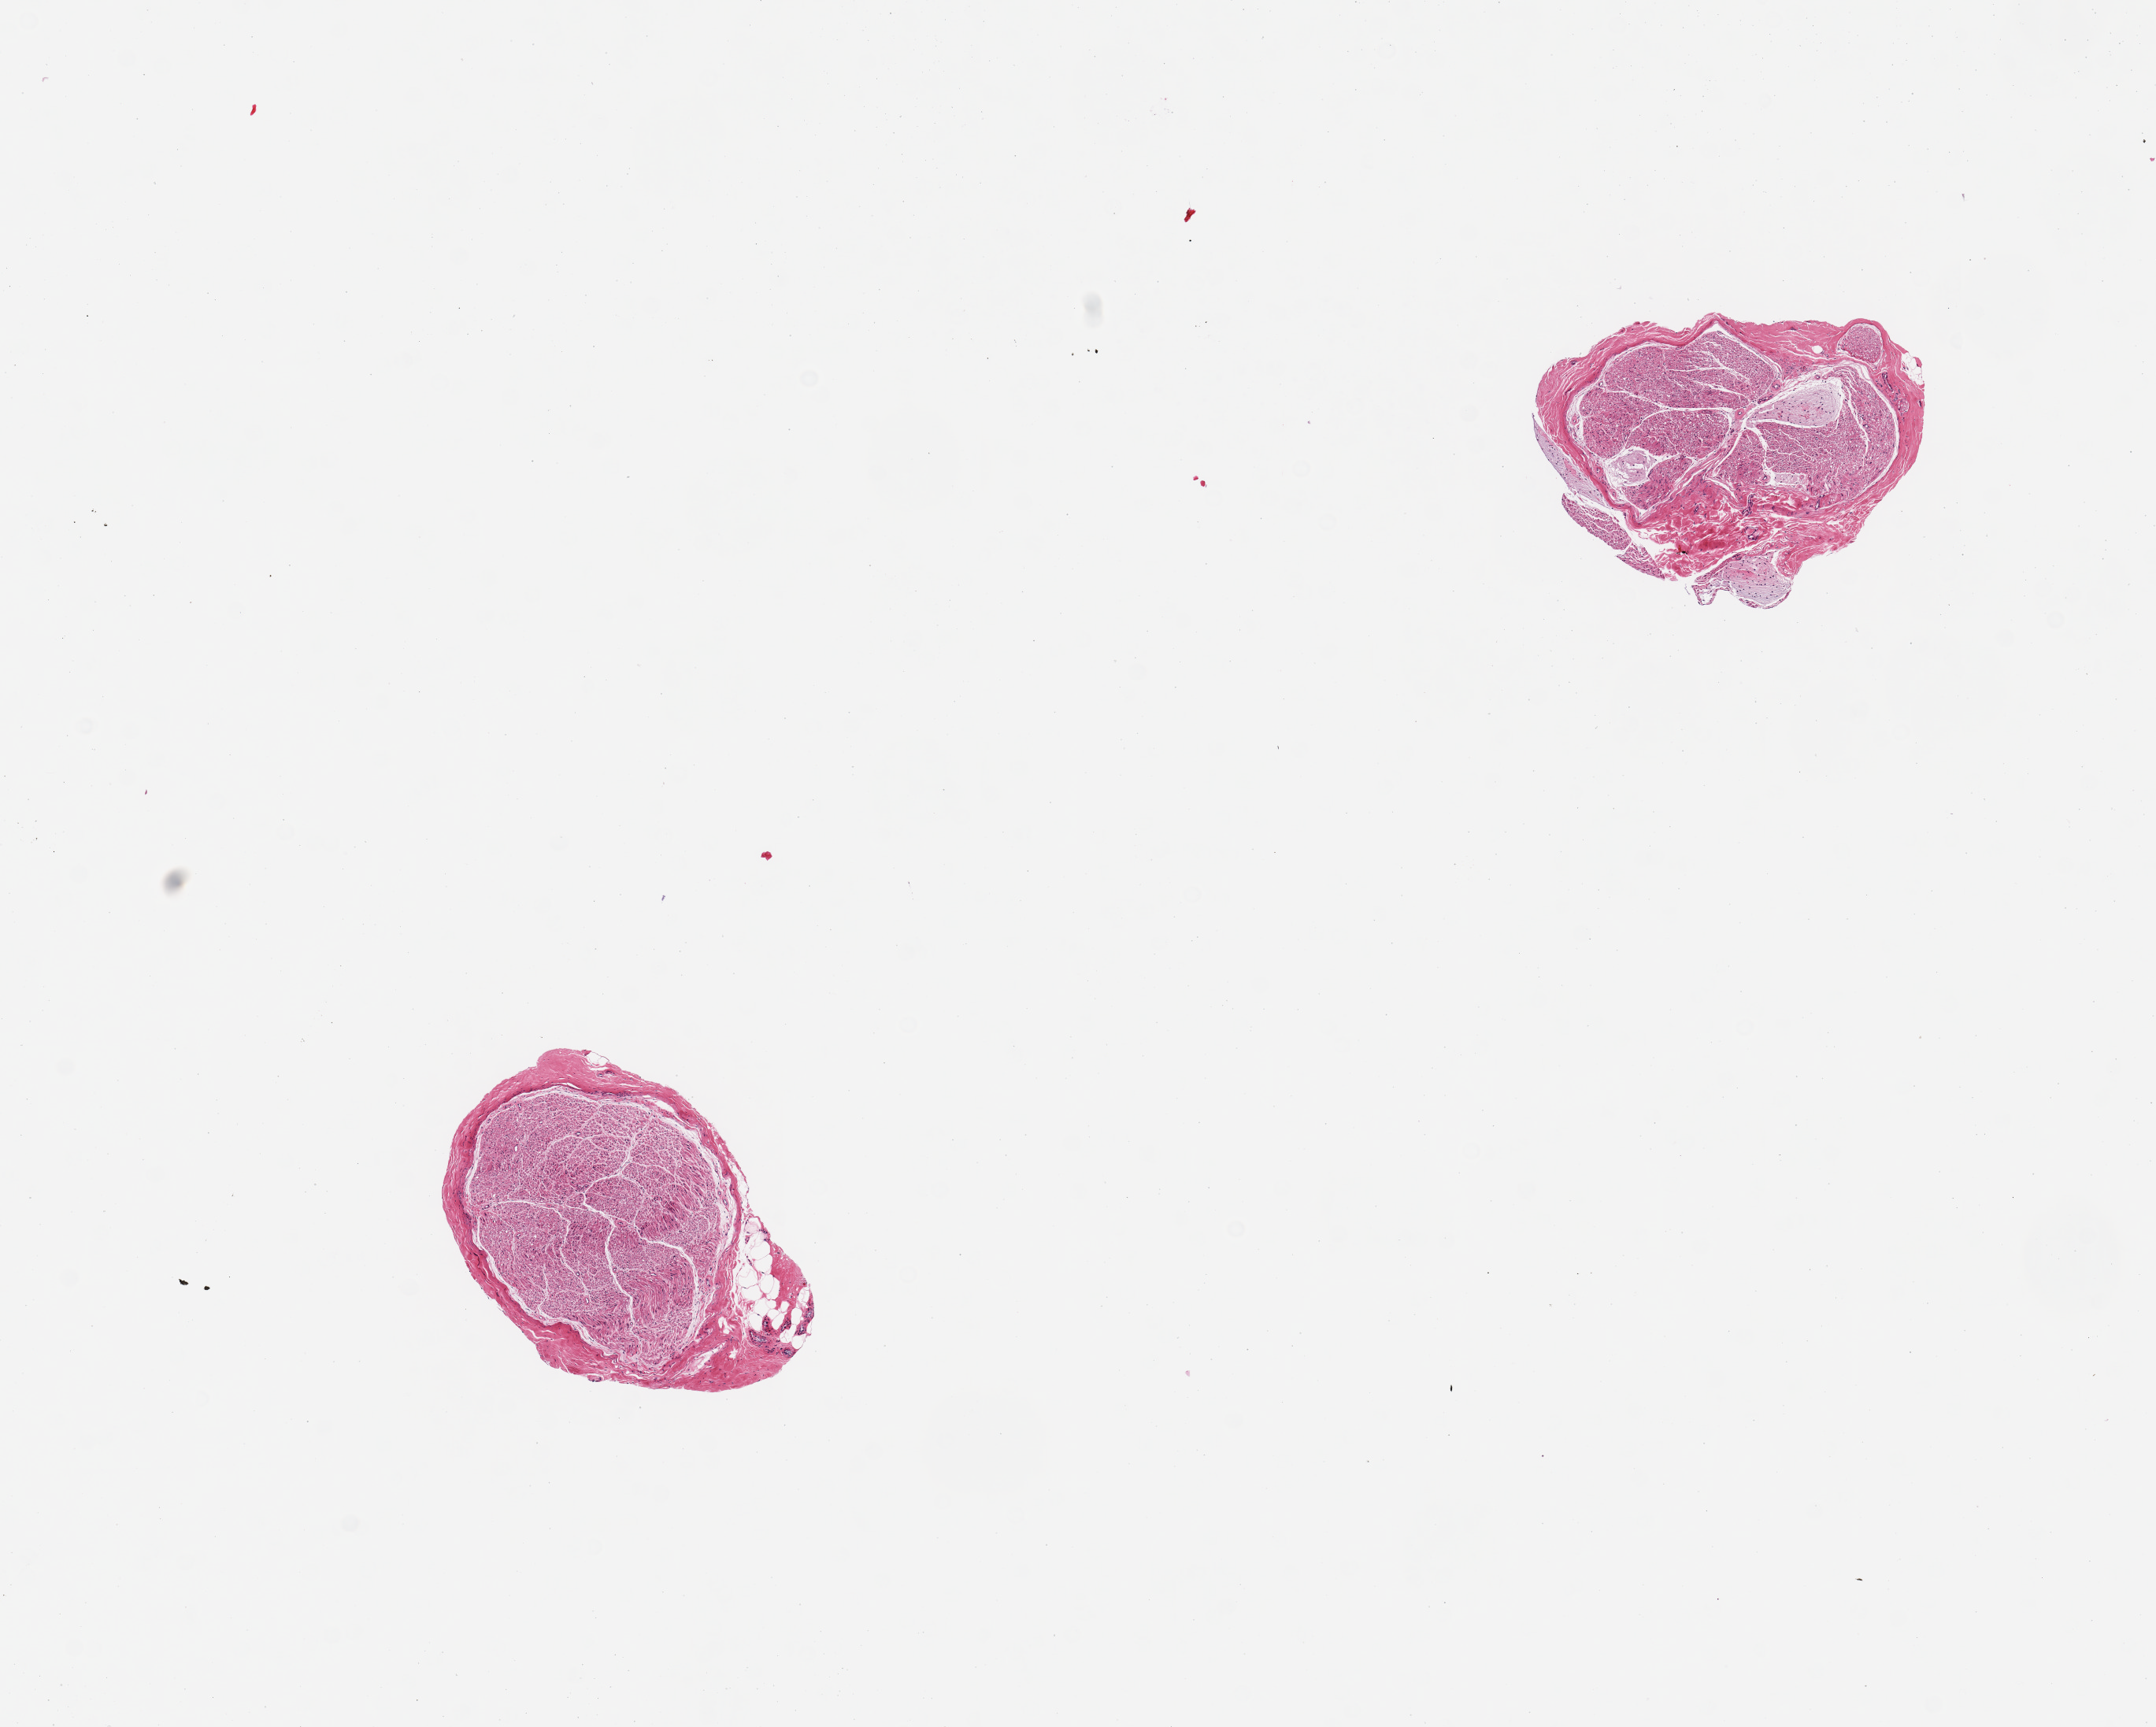
H&E whole-slide image, brightfield — shown as a low-resolution overview of the whole scanned area (about 10.8 x 8.7 mm, acquisition: 20x scan). PAXgene-fixed paraffin-embedded (PFPE) section. Sampled site (target tissue): tibial nerve. Tissue donor sample. Donor: female.
Reviewer comment on this tissue sample: 2 pieces; 1 with several edematous nerve bundles.